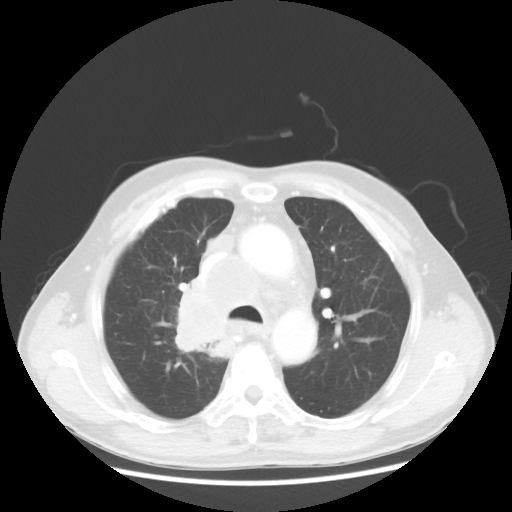
Chest CT, one axial slice. Position 83 of 124 along the scan axis. Reconstruction kernel STANDARD. 100 kVp. Lung window (W 1500 / L -600 HU). 512 × 512 image matrix, field of view 382 × 382 mm. Patient: male, 64 years. Case-level facts recorded for this patient, not image findings: clinical TNM (as recorded): T3 N3 M0.
Annotated regions visible in this slice (rectangle marked by the reading radiologist):
- lung tumour (recorded histology: small cell carcinoma): bounding box <173,277,241,365> (left, top, right, bottom; pixels)